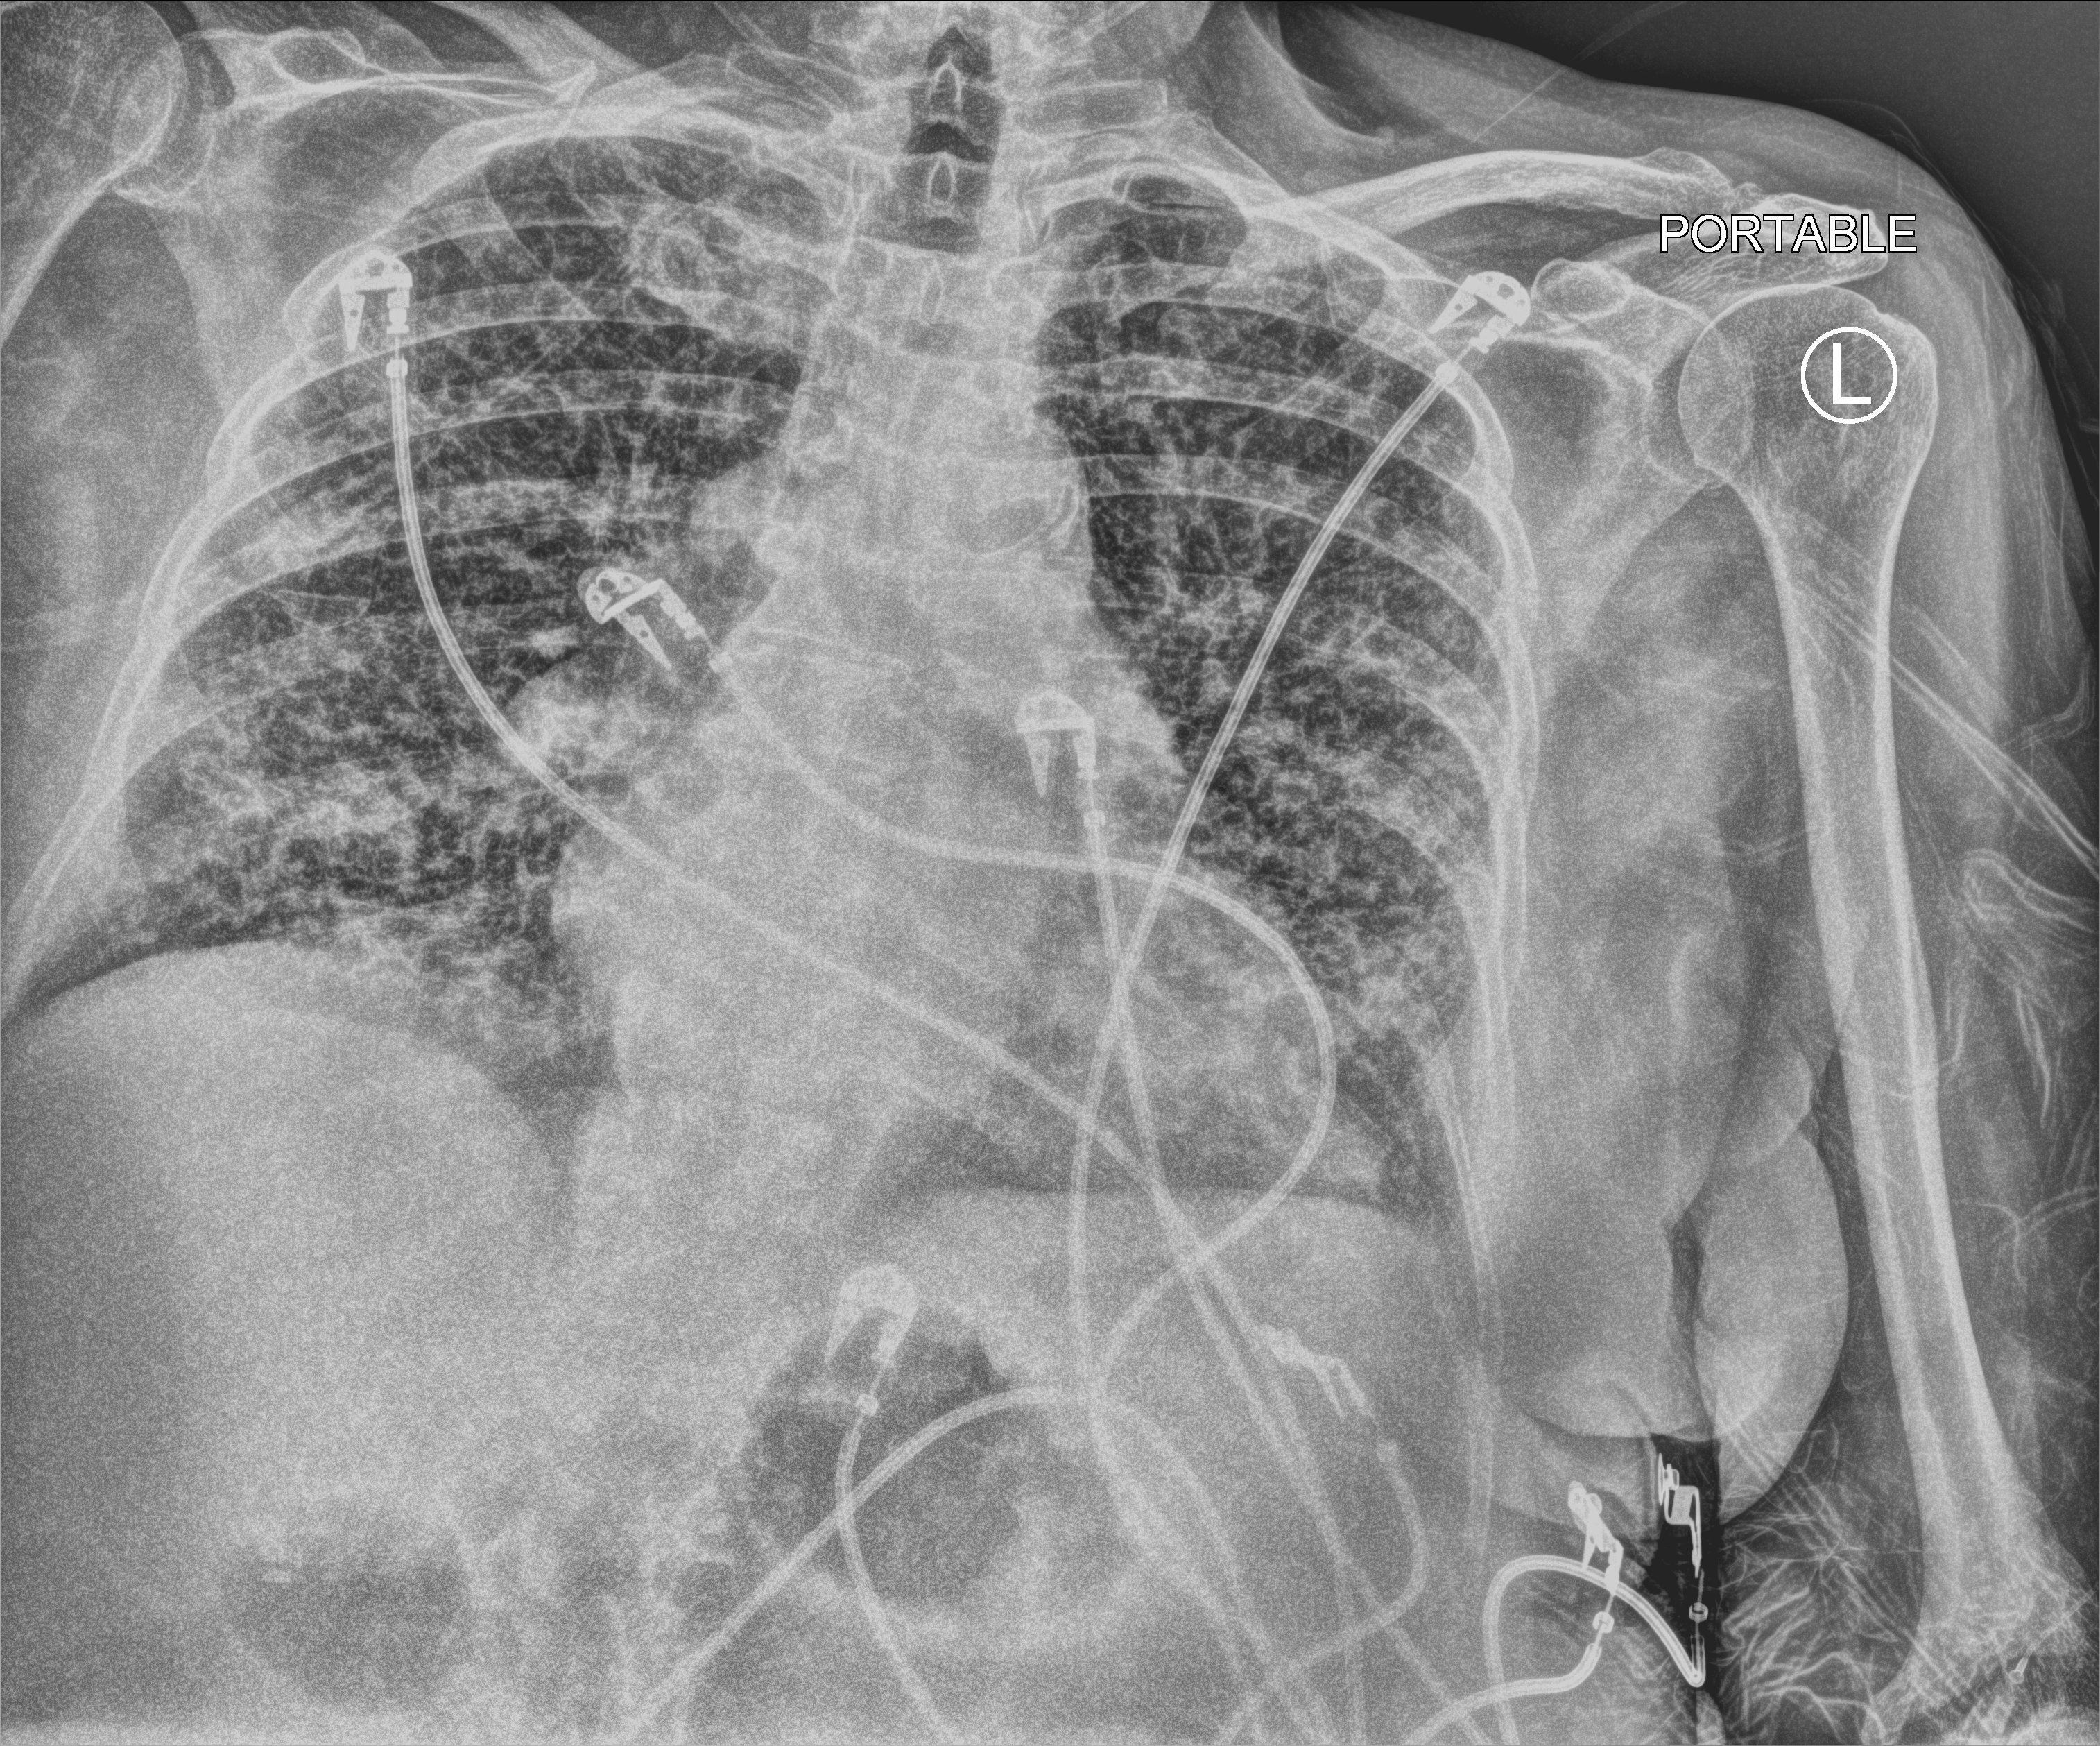
Bedside chest radiograph (computed radiography), anteroposterior (AP) projection. Patient hospitalised with COVID-19; female, aged 75–90 years.
From the hospital-stay record, not from the radiograph (when in the stay this image was taken is not recorded): mechanically ventilated during this hospital stay: no.